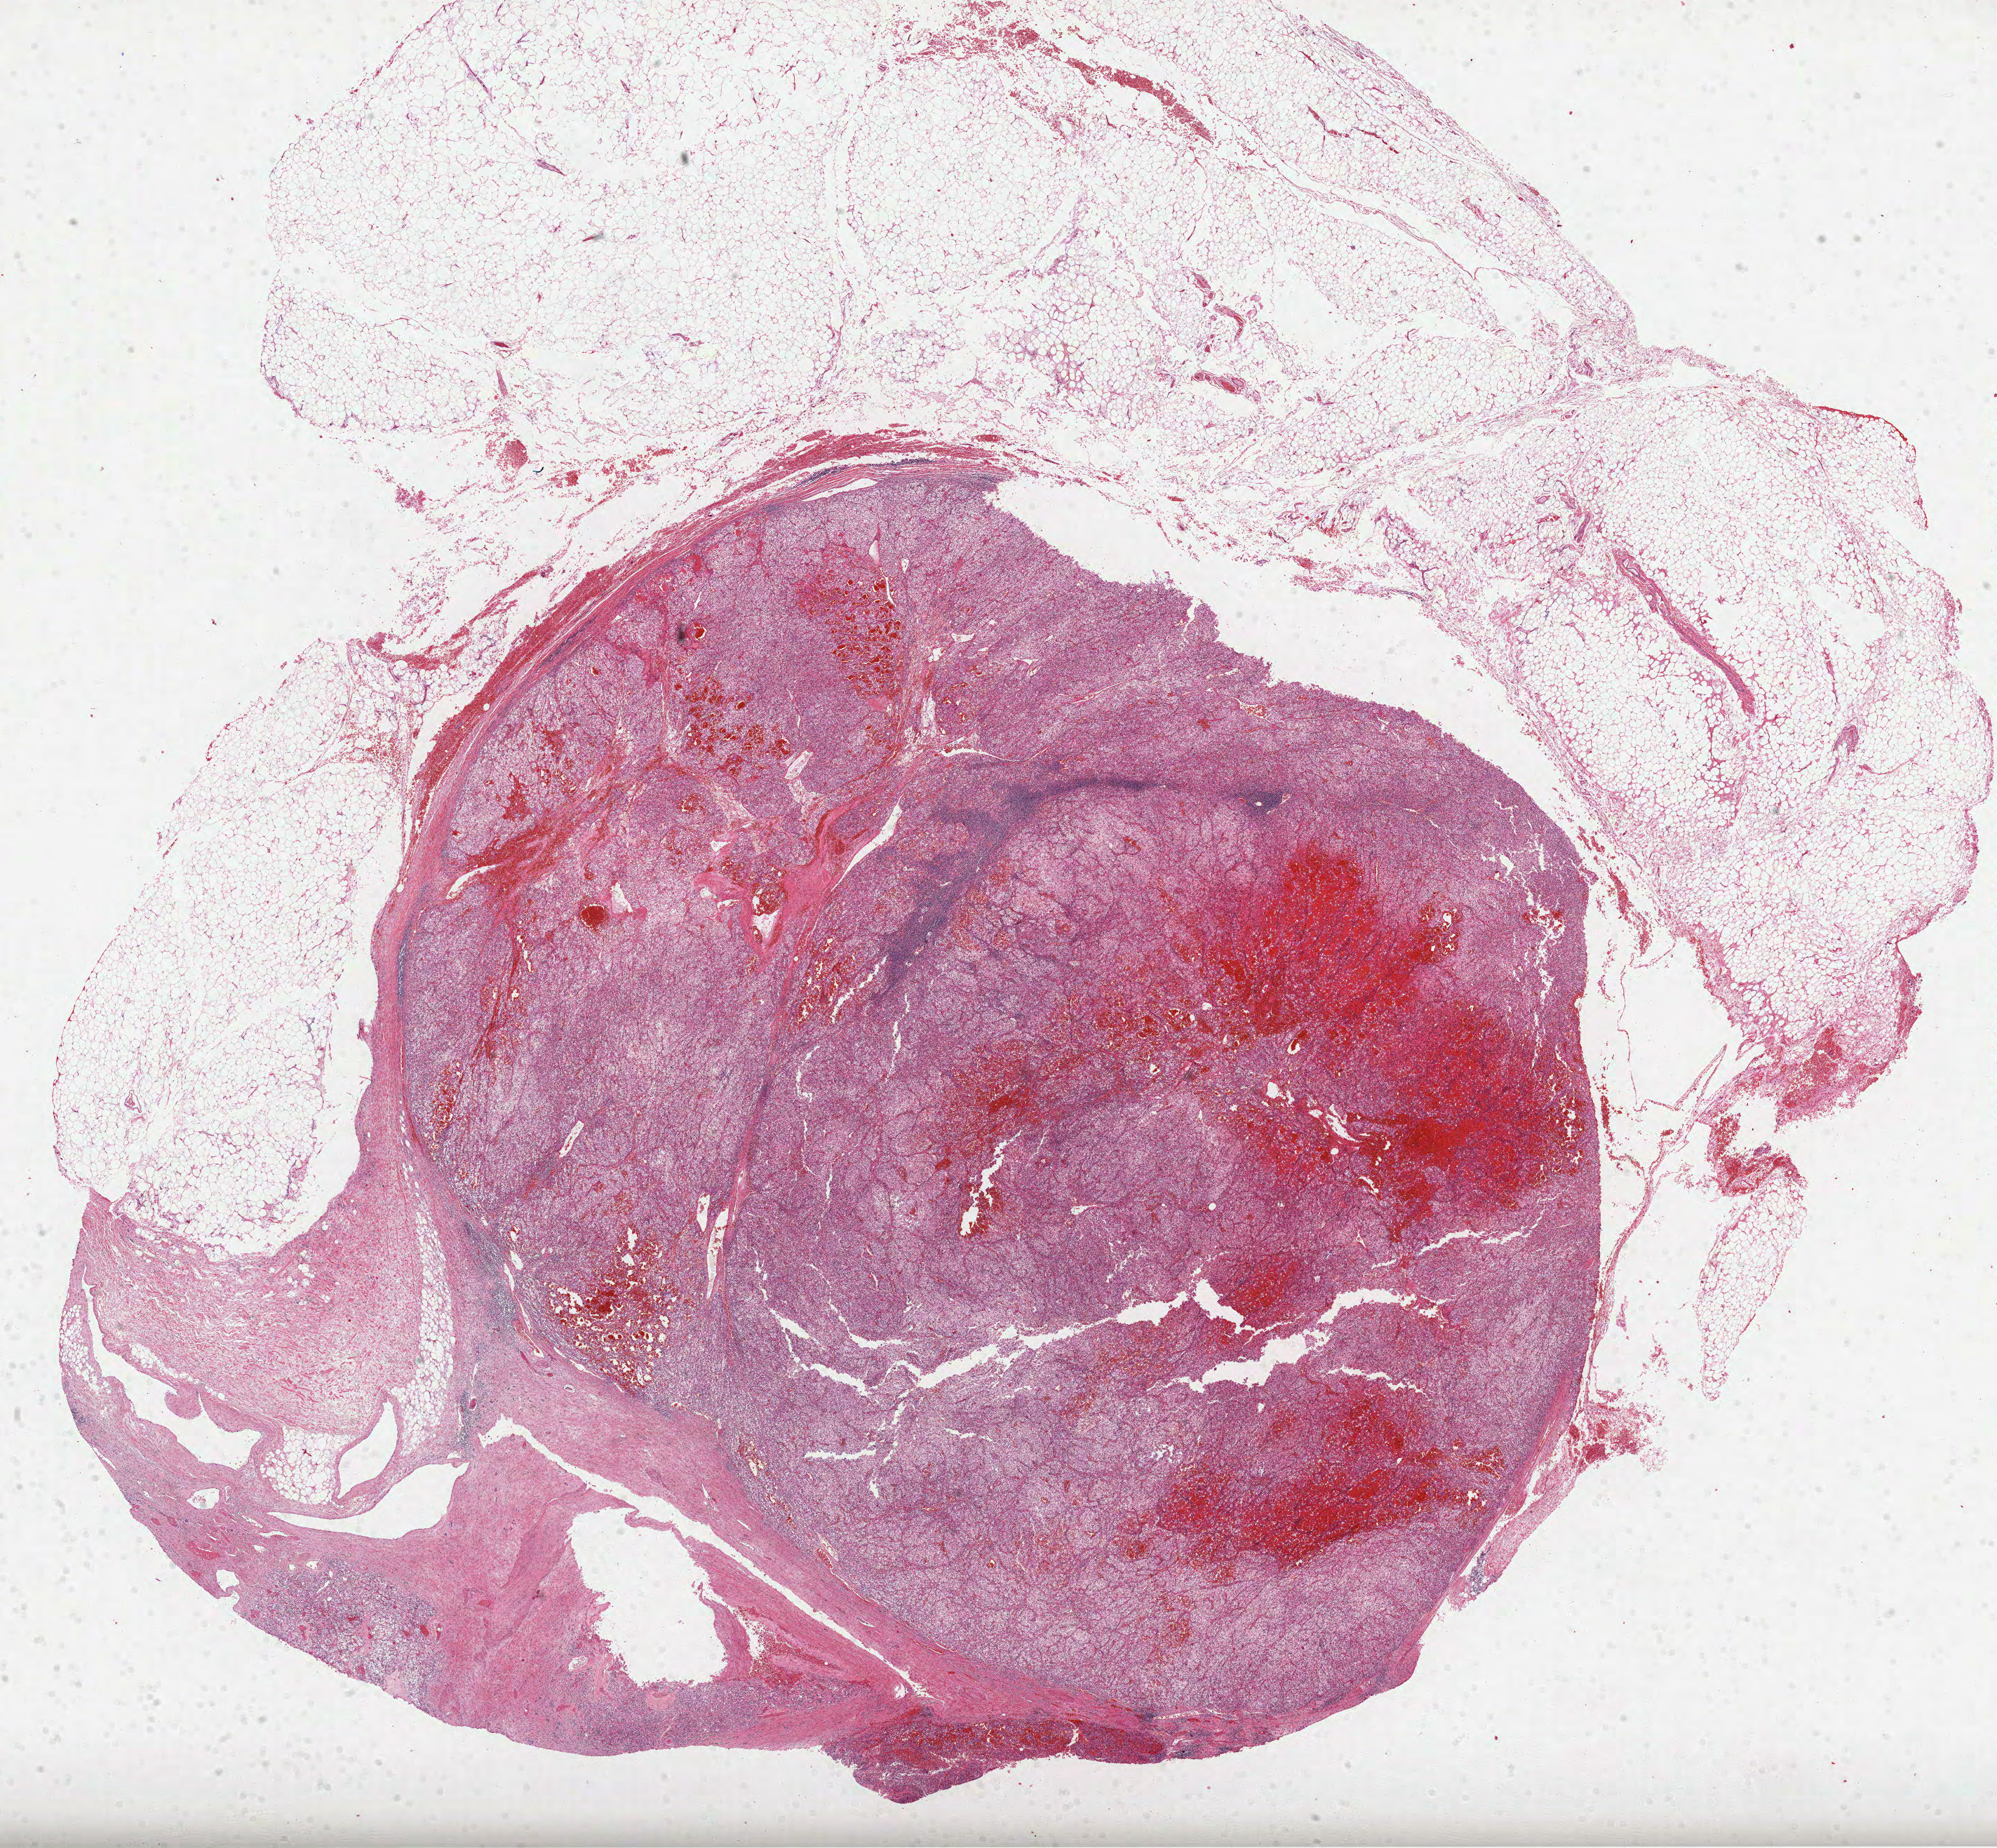
Digitized Hematoxylin and eosin (H&E) stained tissue section (whole slide), low-resolution overview of the scanned area, about 23.0 x 21.3 mm (from a 40x scan); formalin-fixed paraffin-embedded (FFPE) diagnostic section; sample: primary tumour, kidney. Female, age 66 years at initial diagnosis. Histologic grade: G3 (poorly differentiated).
* laterality: right
* AJCC pathologic stage: III (6th edition)
* diagnosis: Clear cell adenocarcinoma, NOS